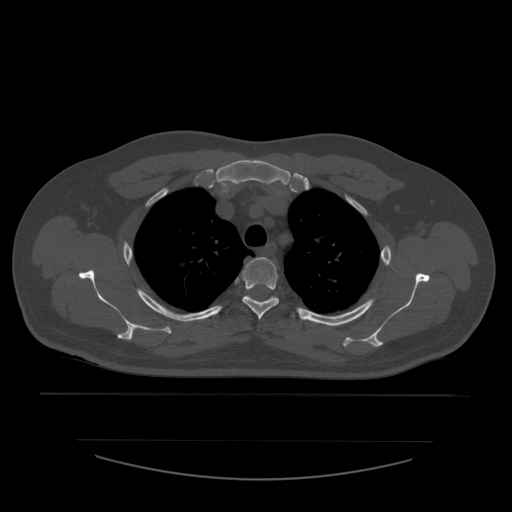
CT including the spine, one axial slice. Reconstruction kernel STANDARD. Bone window (W 1800 / L 400 HU). 1.25 mm slice thickness. 512 × 512 image matrix. Patient age 44 years. Case-level facts recorded for this patient, not image findings: primary cancer: soft tissue sarcoma.
Structures marked on this image (semi-automatic segmentation, software-assisted and operator-edited):
- T3 vertebra: bounding box [x1, y1, x2, y2] px = [242, 257, 280, 320]
- T4 vertebra: [248, 296, 295, 317]